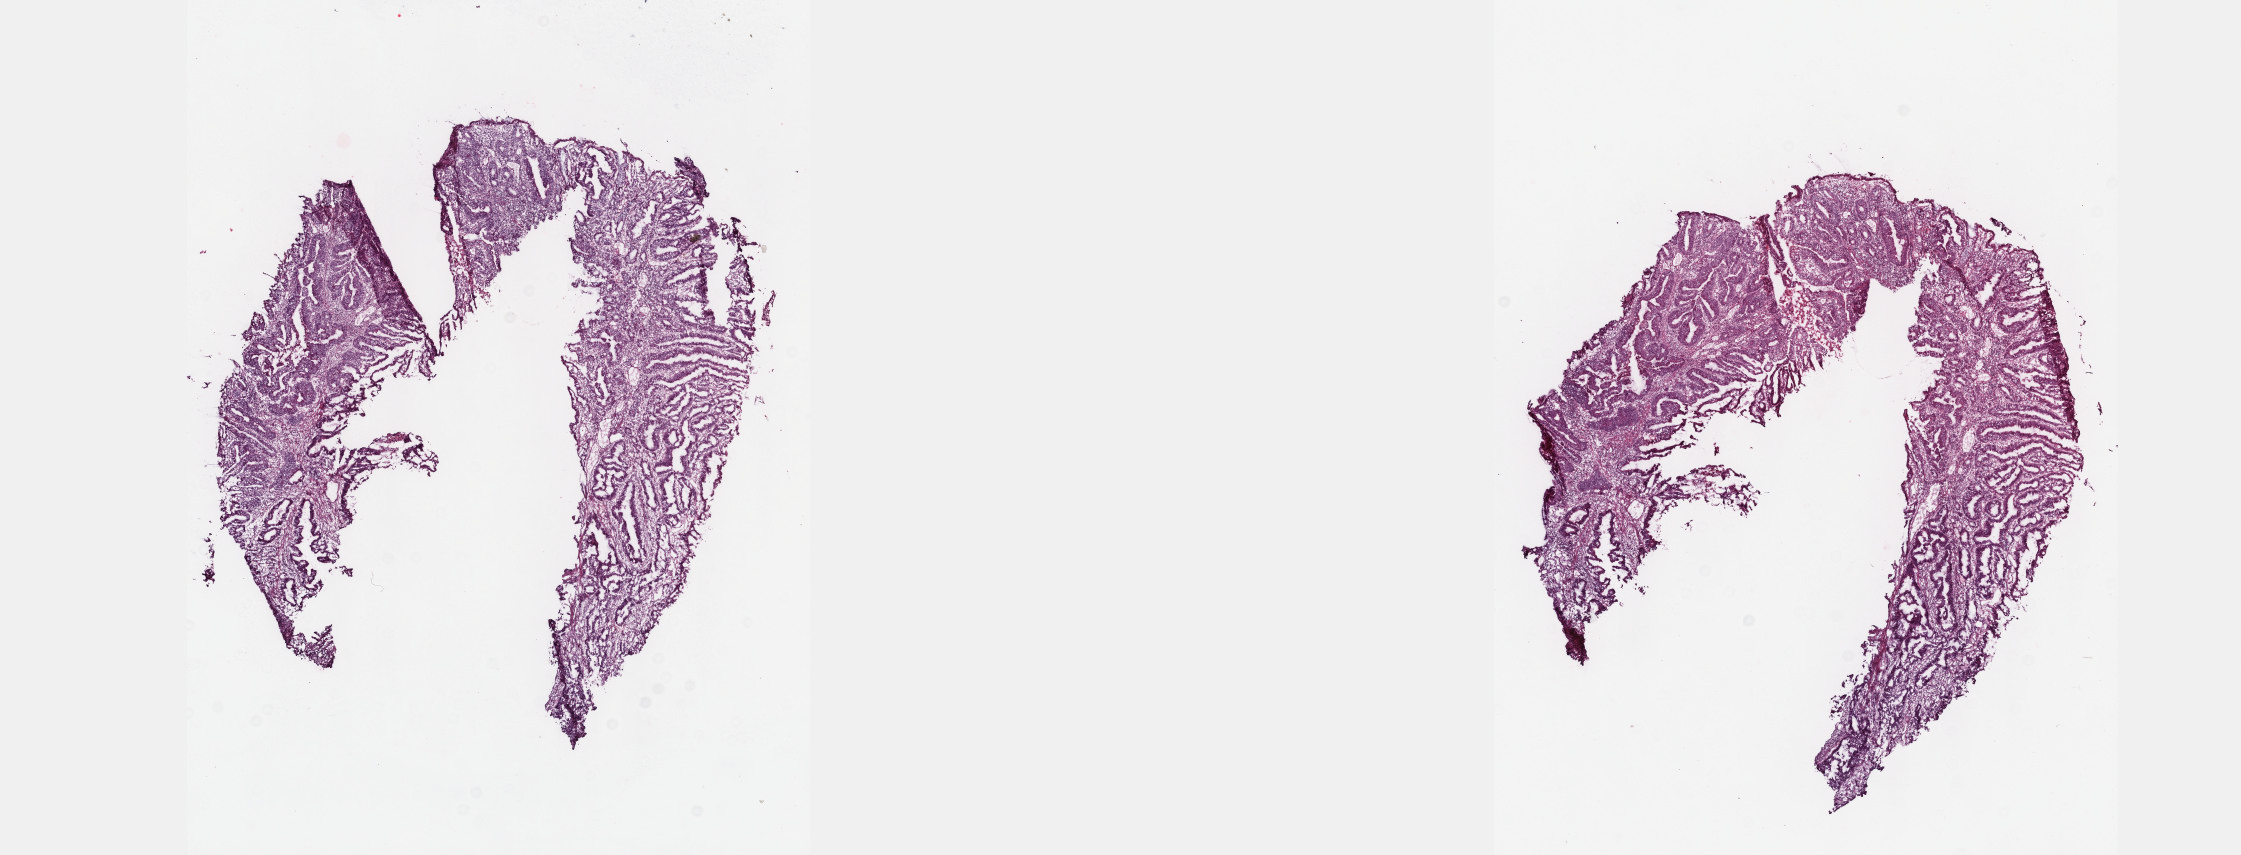
Whole-slide histology image, H&E-stained — low-resolution overview of the scanned area, about 18.1 x 6.9 mm. Frozen section. Primary tumour sample from the rectum. Patient: male, age at initial diagnosis 68 years. Composition of this section per pathologist review: tumour cells 73%, tumour nuclei 65%, normal cells 10%, stromal cells 15%, necrosis 2%. Inflammatory infiltration, as recorded: lymphocyte infiltration 23%, monocyte infiltration 6%, neutrophil infiltration 4%.
Lymph nodes positive (case pathology): 2 of 16 examined. Diagnosis: Adenocarcinoma, NOS. AJCC pathologic stage: IIIB (6th edition).